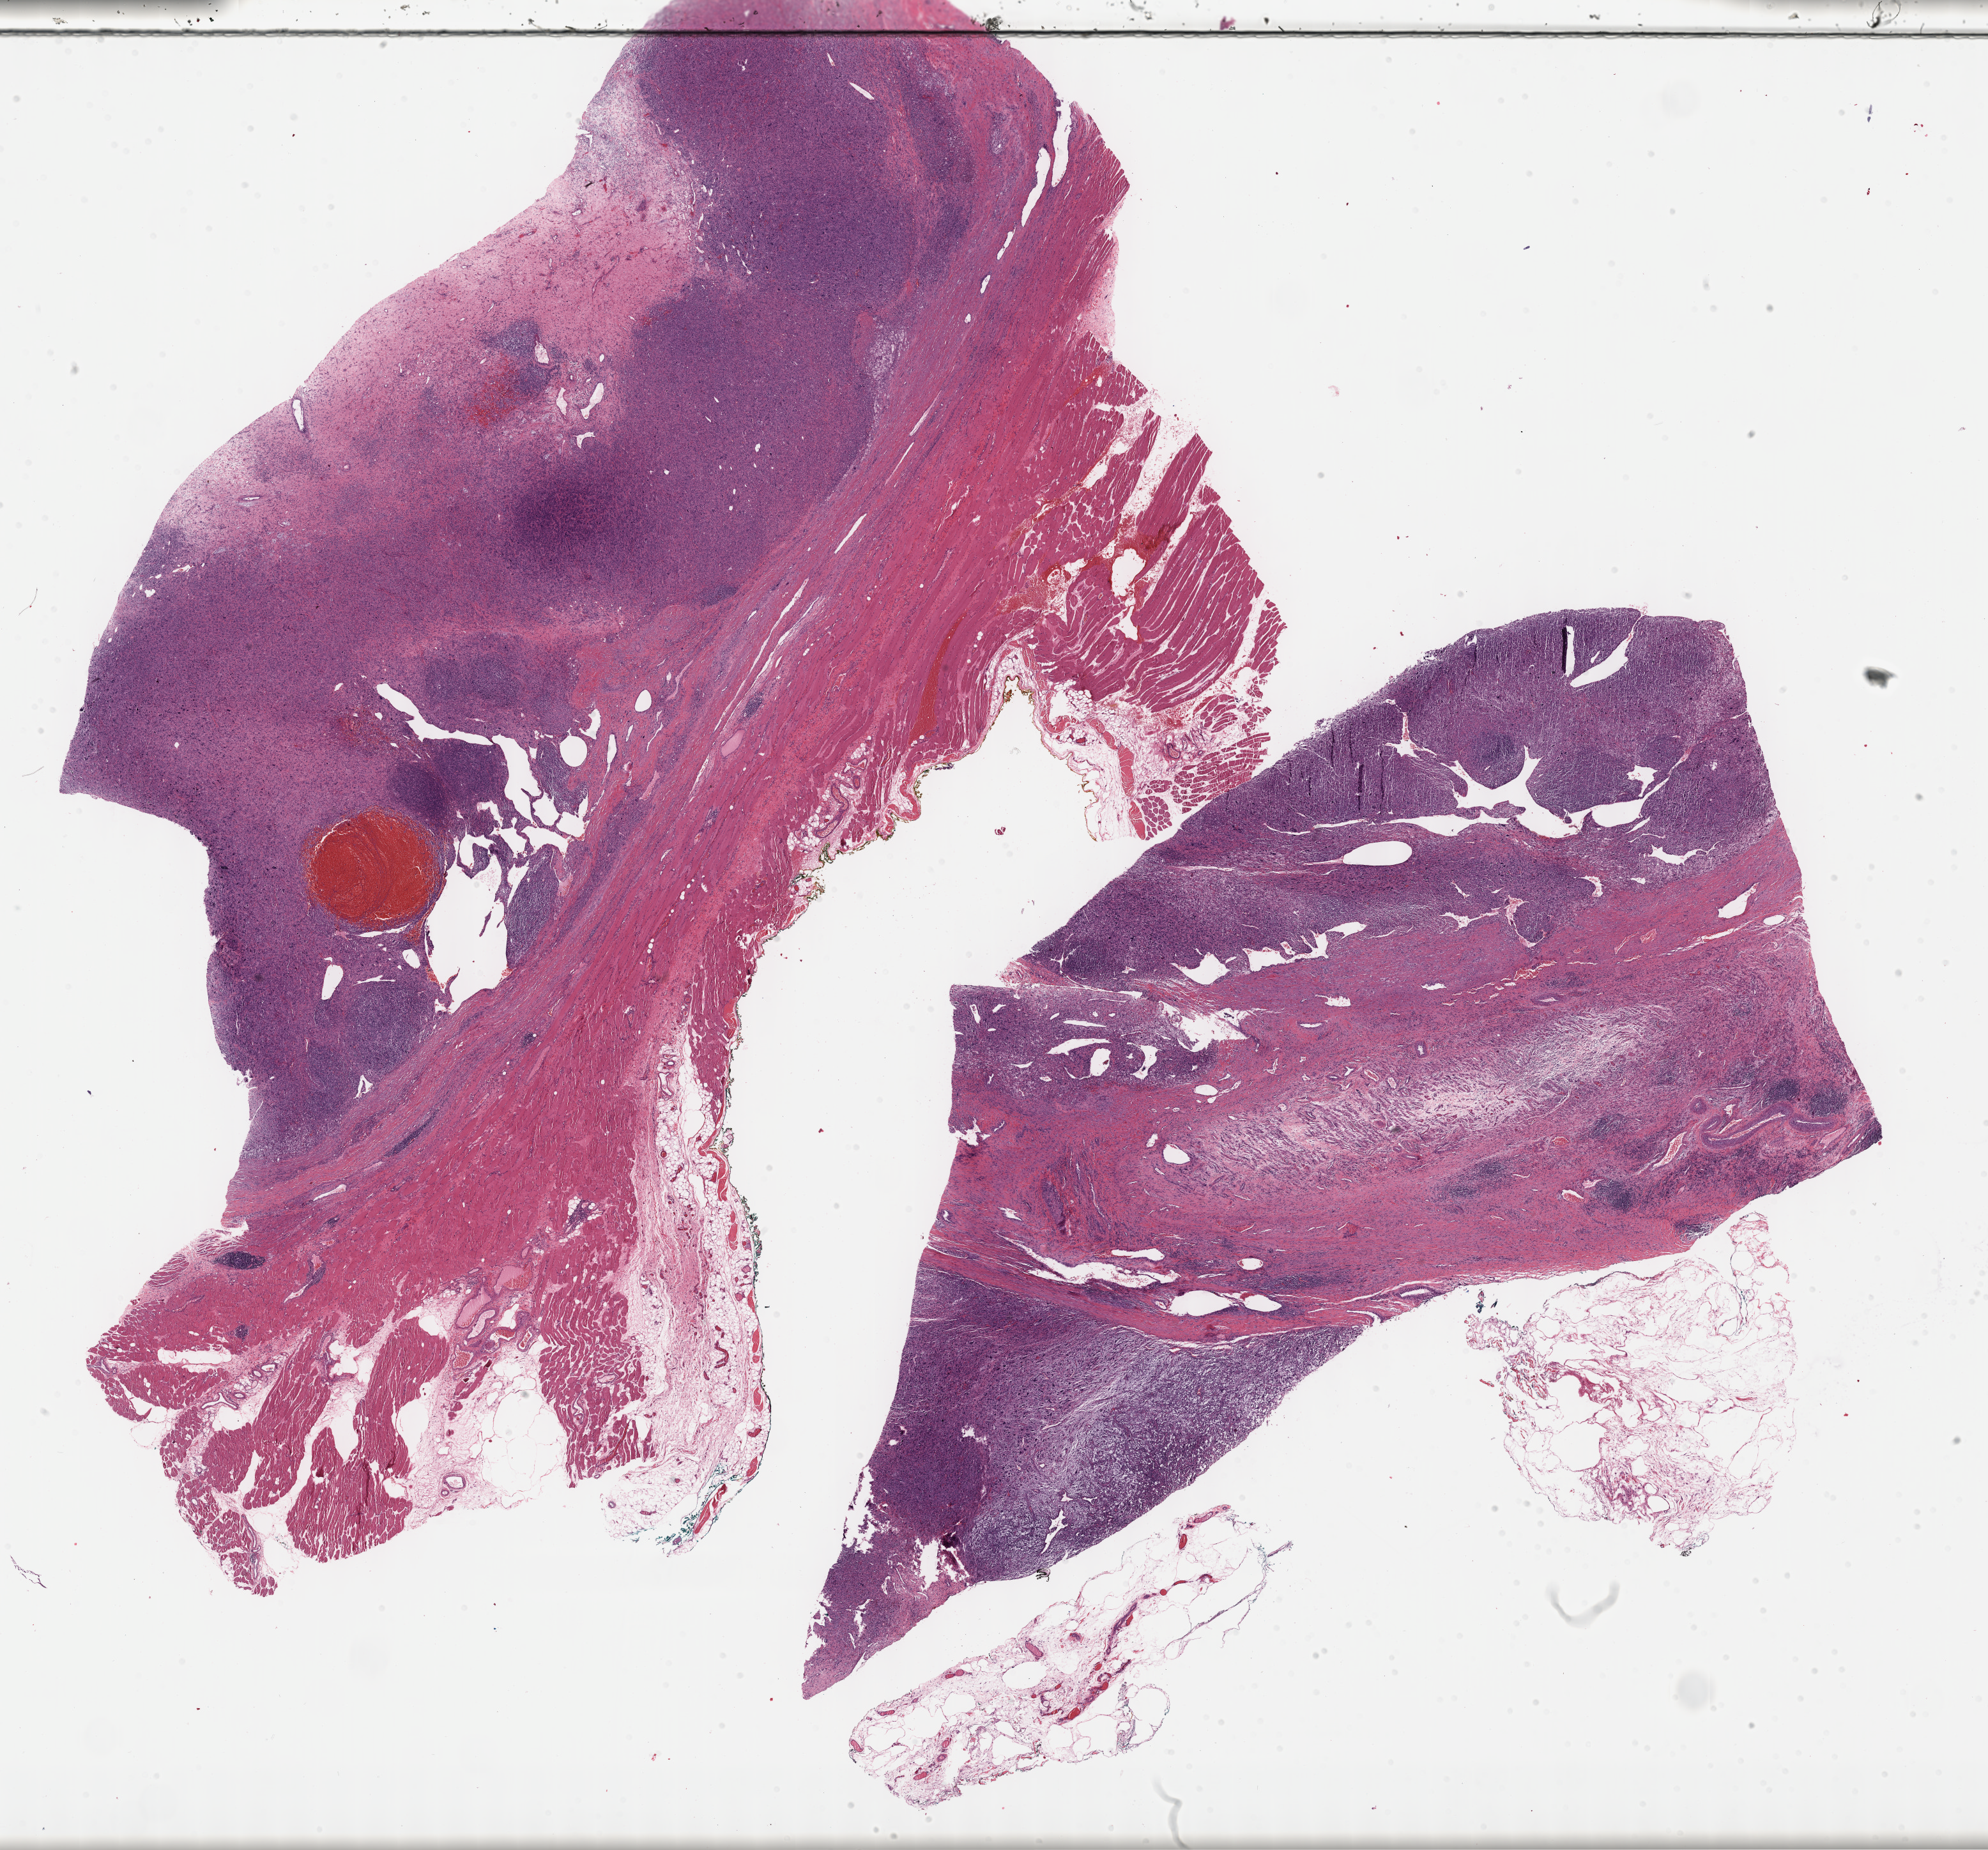
Digitized H&E-stained tissue section (whole slide) — whole scanned area (about 25.2 x 23.4 mm, slide scanned at 40x) shown as a low-resolution overview, FFPE section, sample: primary tumour, connective, subcutaneous and other soft tissues. Male, age 51 years at initial diagnosis.
Pathologic diagnosis: Fibromyxosarcoma (connective, subcutaneous and other soft tissues of thorax).